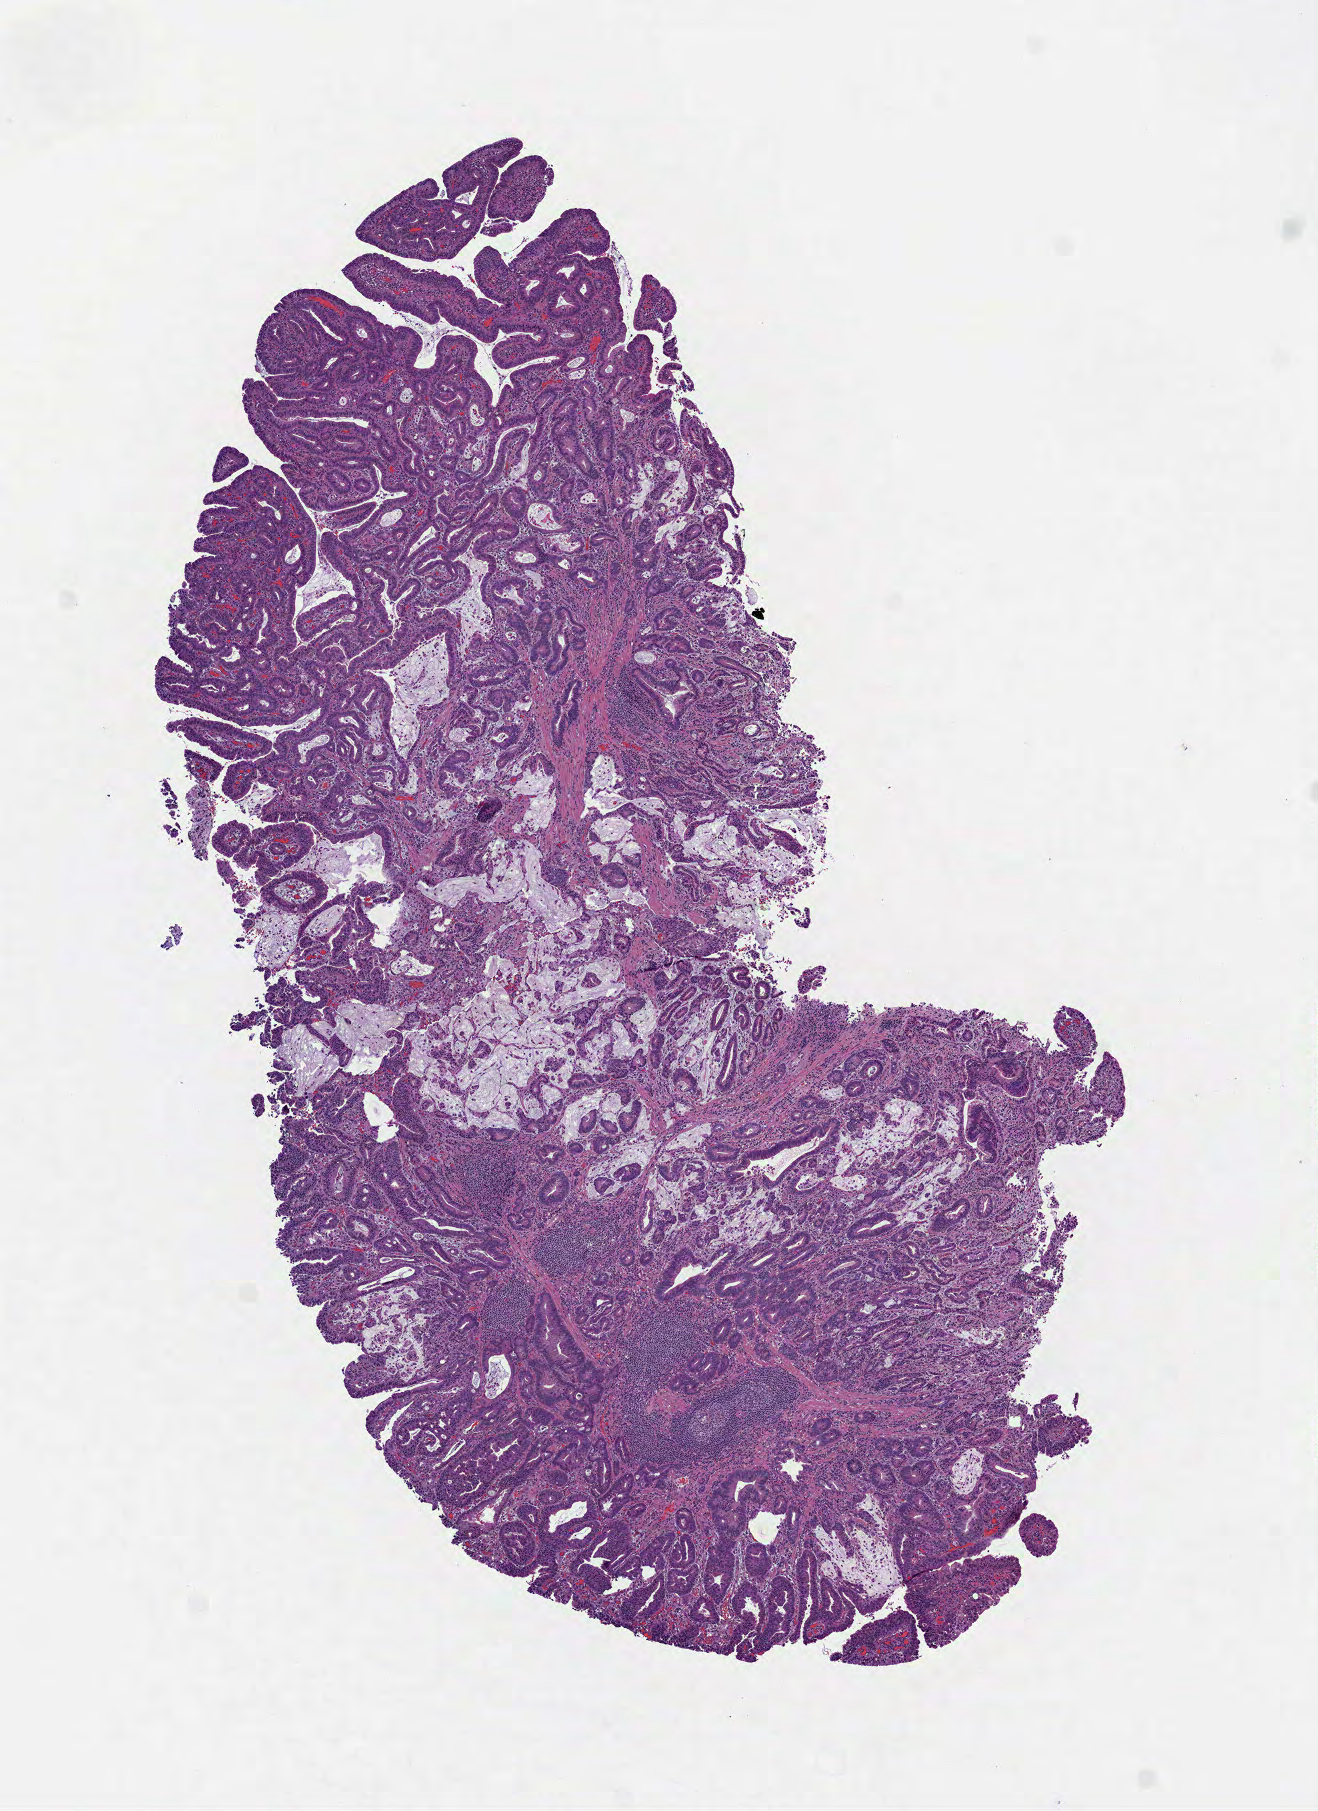
Digitized H&E tissue section (whole slide), whole scanned area (about 5.3 x 7.3 mm) shown as a low-resolution overview, FFPE section, primary tumour sample from the stomach. Patient: male, age at initial diagnosis 77 years.
Histologic diagnosis: Adenocarcinoma, NOS.